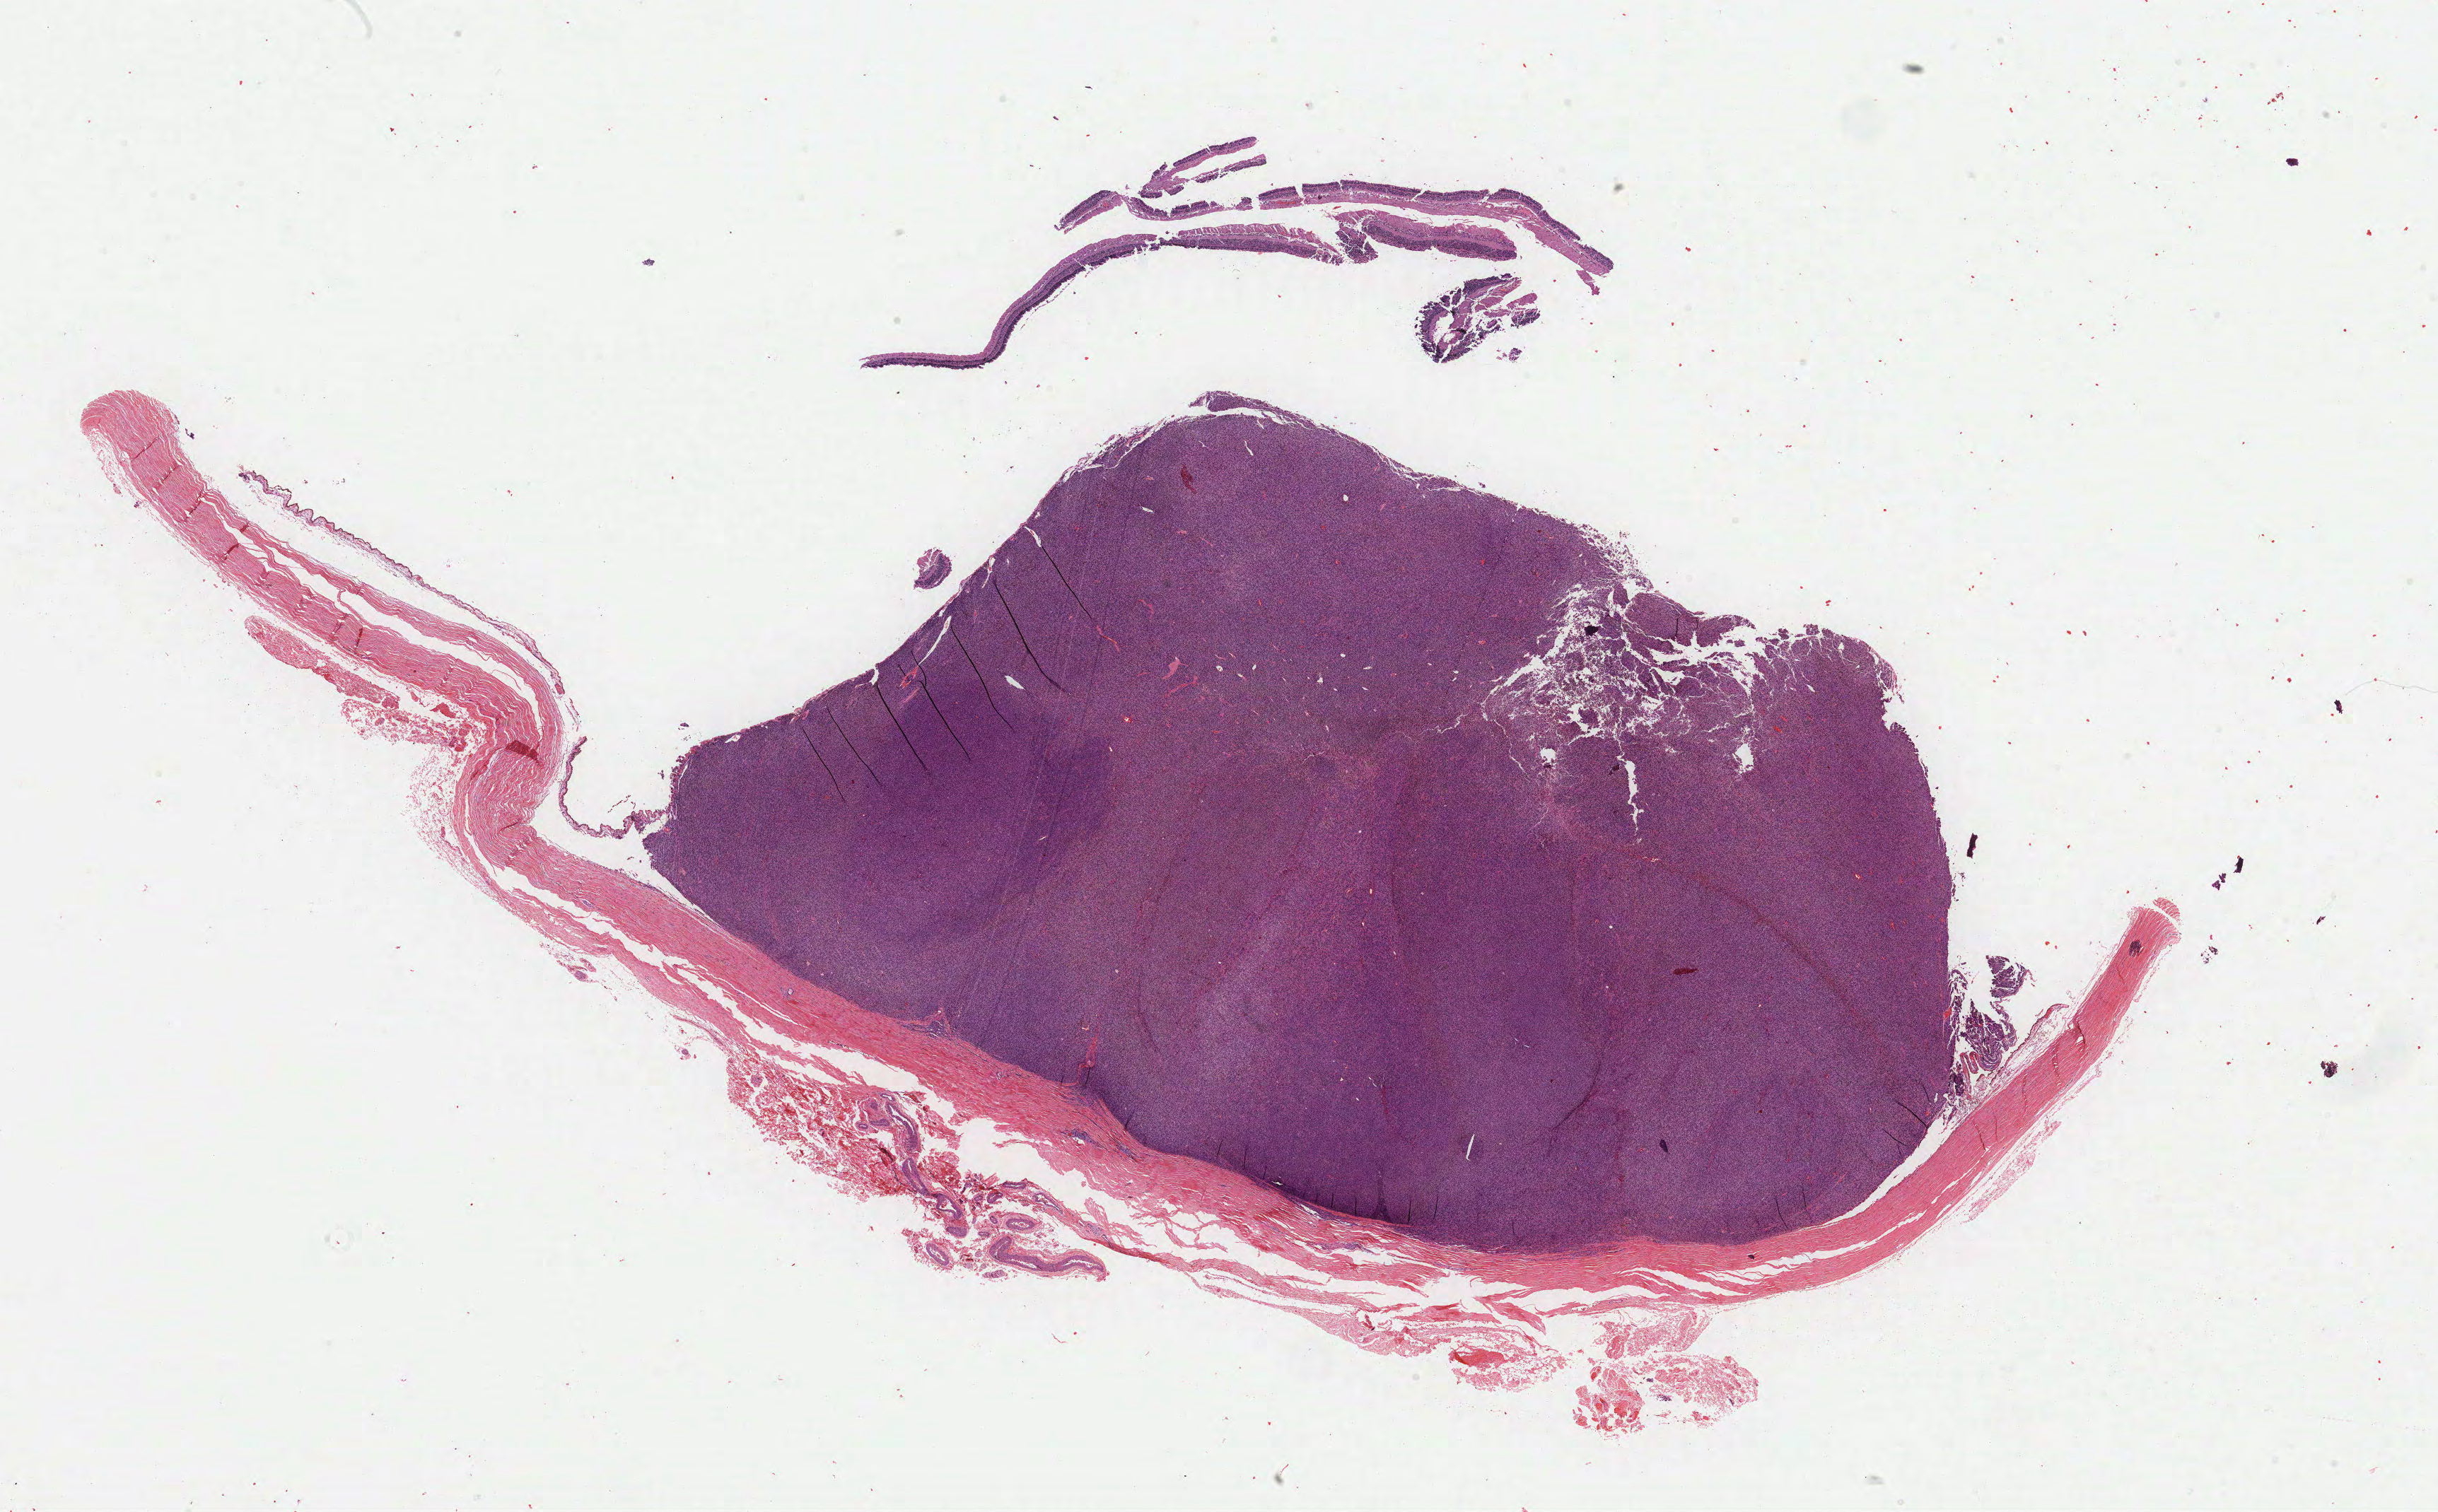
Whole-slide histology image, Hematoxylin and eosin (H&E) stained, whole scanned area (about 27.3 x 16.9 mm, acquisition: 40x scan) shown as a low-resolution overview. Formalin-fixed paraffin-embedded (FFPE) diagnostic section. Primary tumour sample from the uvea. Patient: female, age at initial diagnosis 41 years.
• AJCC pathologic stage: IIIA
• diagnosis: Spindle cell melanoma, NOS (choroid)